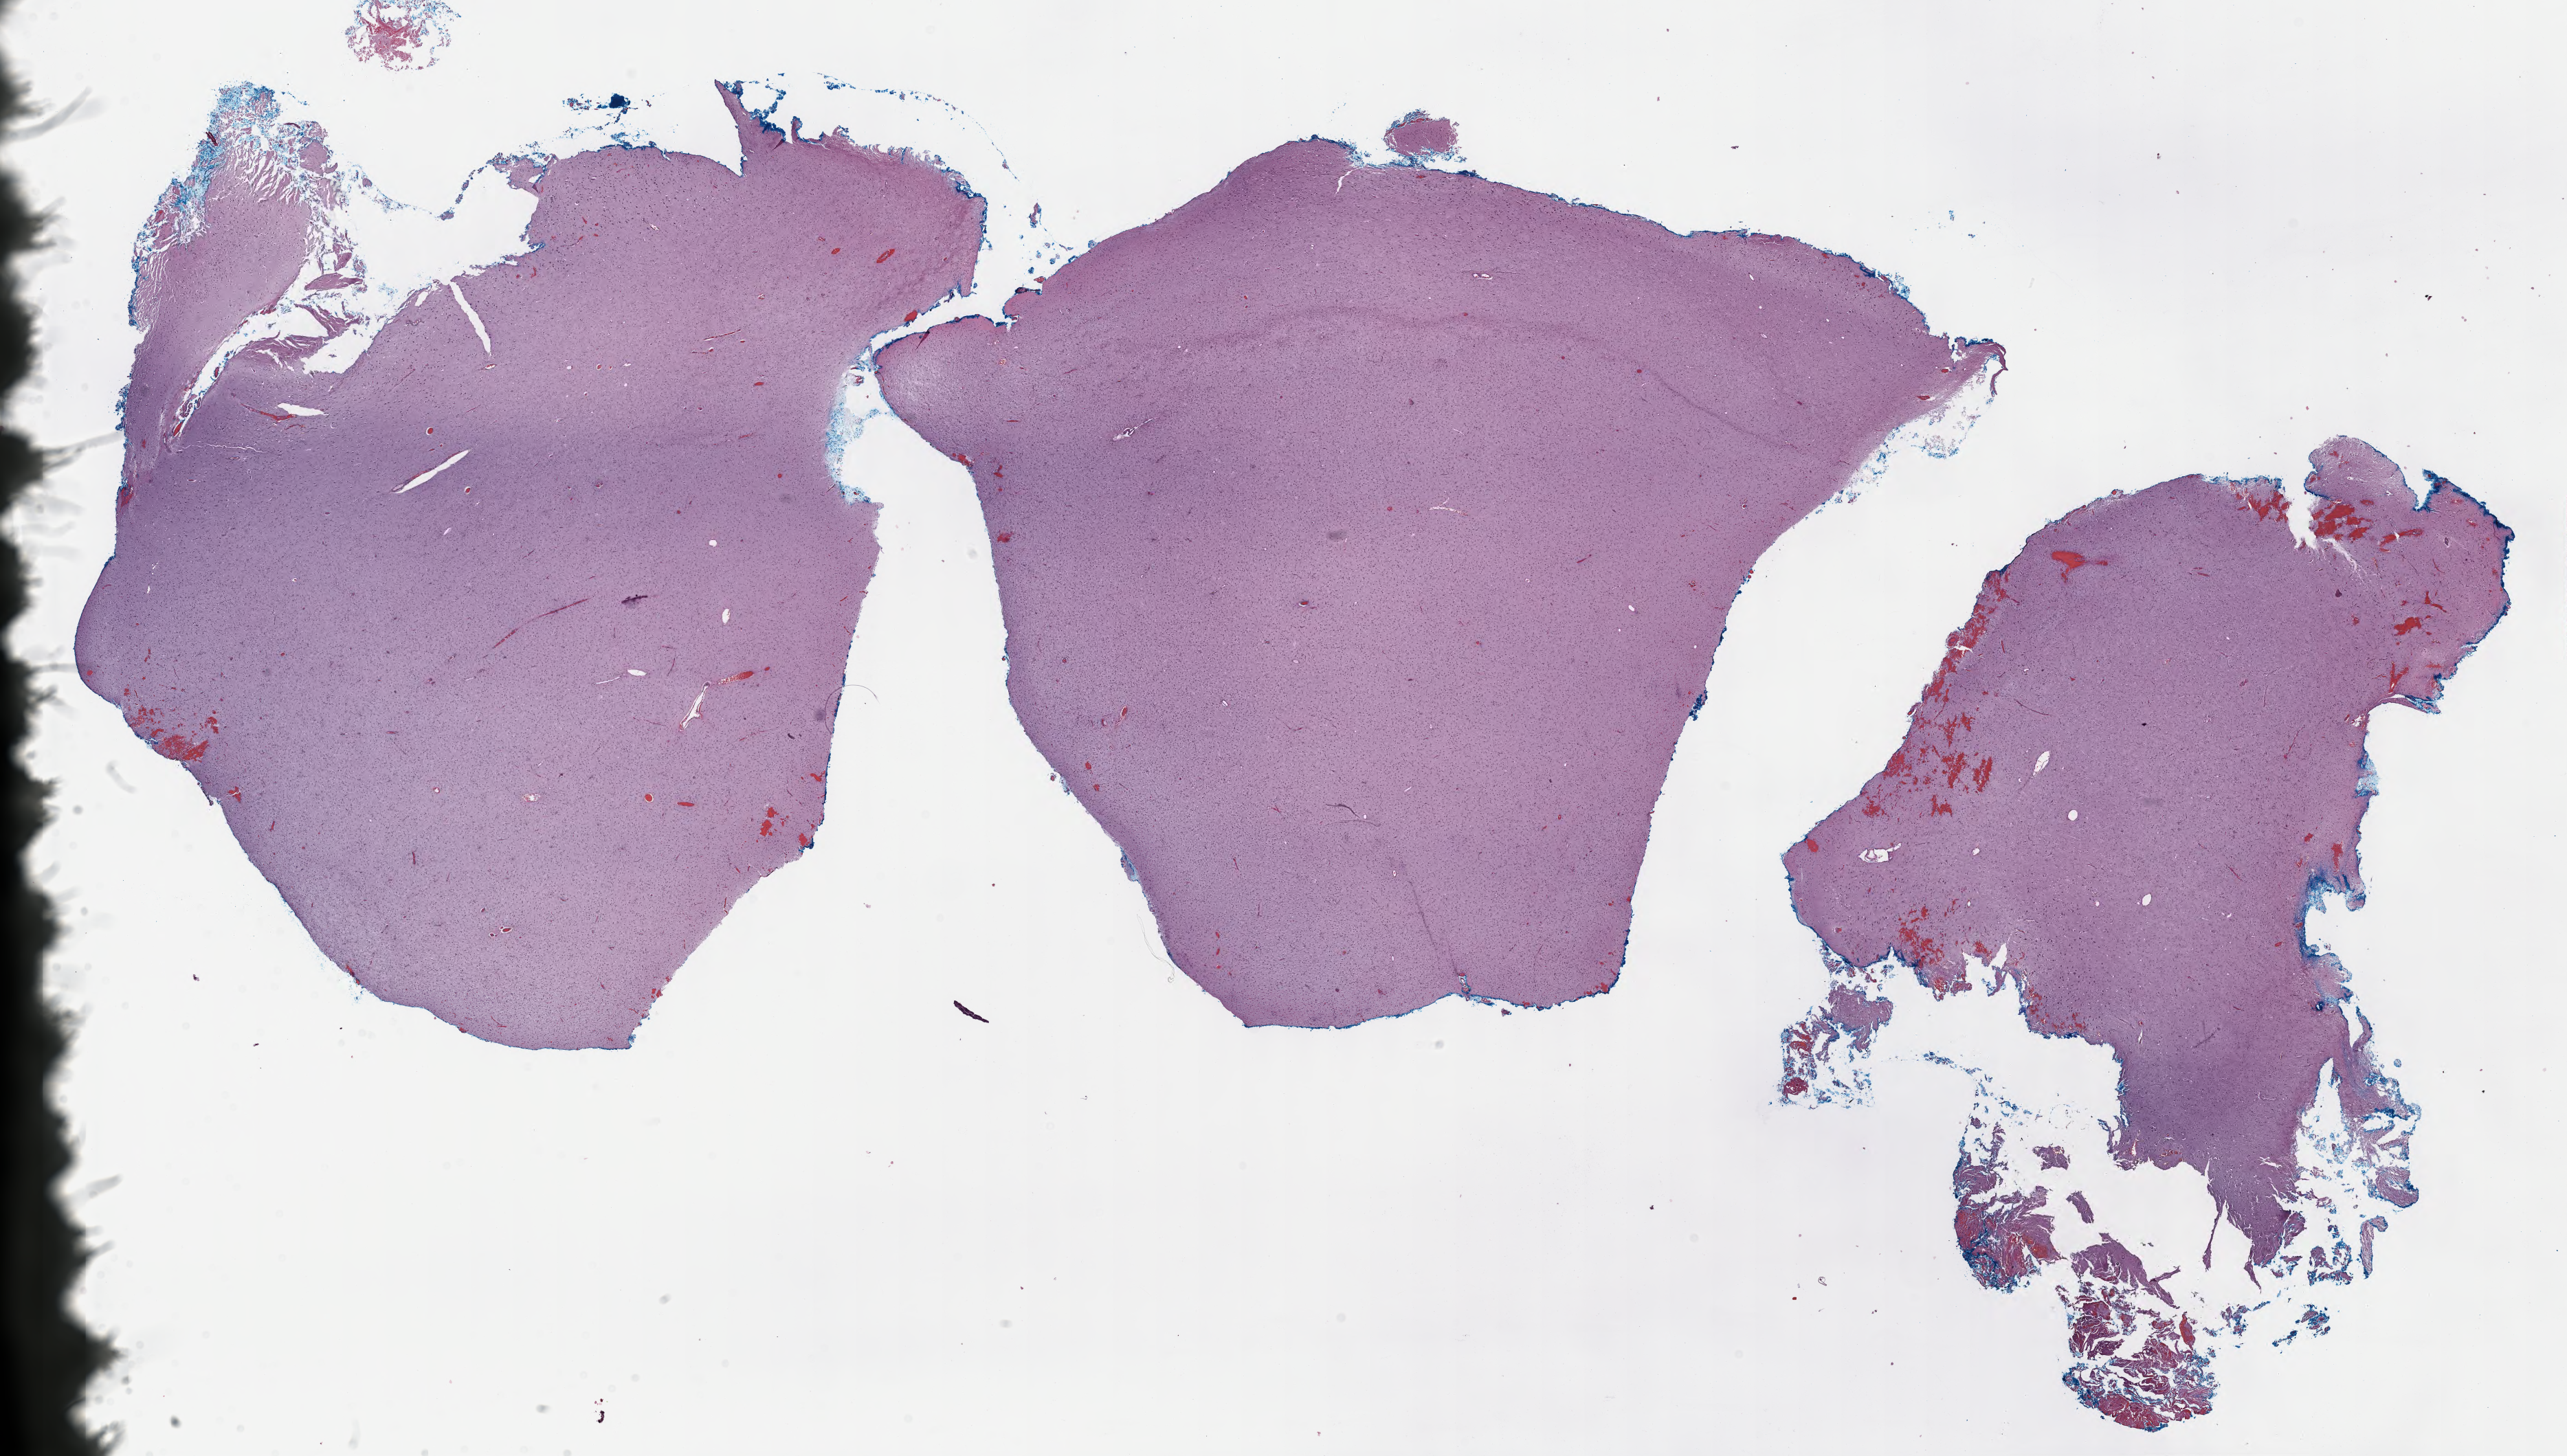
Digitized H&E-stained section of tumor tissue from the frontal lobe — whole scanned area (about 30.2 x 17.1 mm) shown as a low-resolution overview. Formalin-fixed, paraffin-embedded (FFPE) tissue. Female patient, age 84 months.
- diagnosis: Glioma, malignant